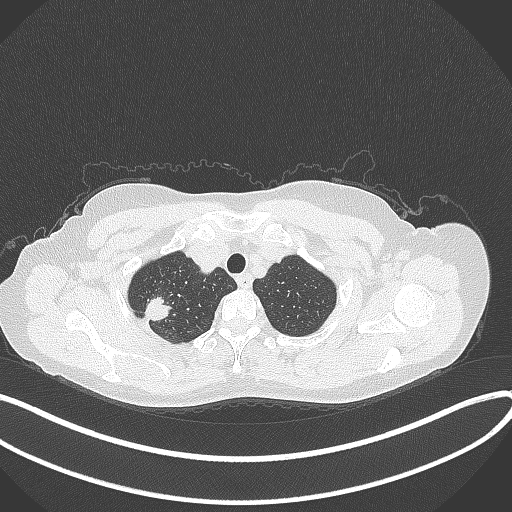
Chest CT, one axial slice. Position 320 of 337 along the scan axis. Lung window (W 1500 / L -600 HU). 1 mm slice thickness. 512 × 512 image matrix, field of view 400 × 400 mm. Patient: female, 50 years. Case-level facts recorded for this patient, not image findings: clinical TNM (as recorded): T1c N0 M0; histopathological grade: G2-3.
Outlined on this slice (bounding box drawn by a radiologist):
- lung tumour (recorded histology: adenocarcinoma): box from (x=137, y=291) to (x=173, y=325) px